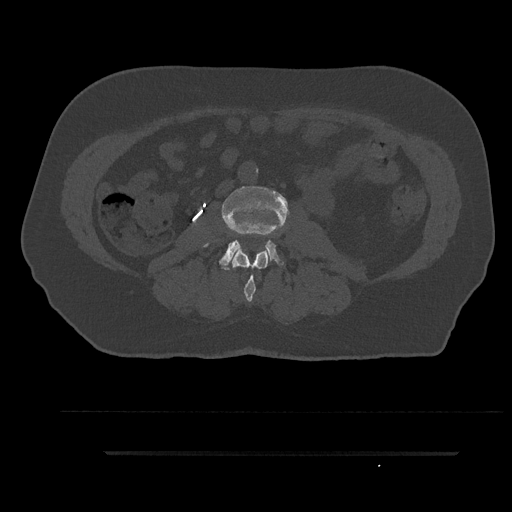
CT including the spine, one axial slice; position 72 of 797 along the scan axis; reconstruction kernel Br40s/3; 120 kVp; bone window (W 1800 / L 400 HU); 0.5 mm slice thickness; 512 × 512 image matrix, field of view 432 × 432 mm. Patient: male, 63 years. Case-level facts recorded for this patient, not image findings: primary cancer: renal; vertebrae with lytic lesions (as recorded): T8.
Outlined on this slice (semi-automatically segmented with operator editing):
- L2 vertebra: box from (x=232, y=250) to (x=268, y=302) px
- L3 vertebra: (x=221, y=185)–(x=288, y=270)